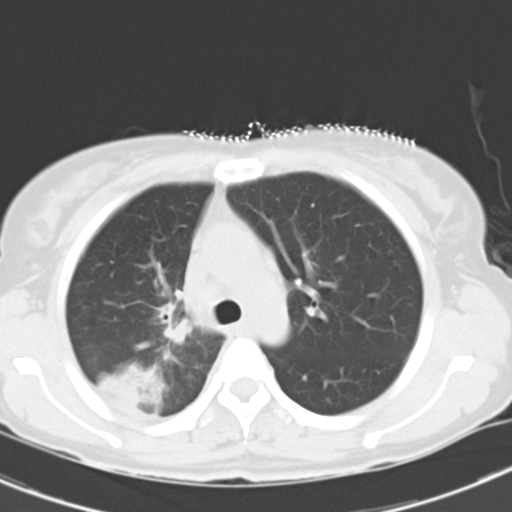
Chest CT, one axial slice. Position 21 of 29 along the scan axis. 120 kVp. Lung window (W 1500 / L -600 HU). 512 × 512 image matrix, field of view 300 × 300 mm. Patient: female, 47 years. From the clinical record (not read from this slice): clinical TNM (as recorded): T1c N3 M0.
Structures marked on this image (bounding box drawn by a radiologist):
- lung tumour (recorded histology: adenocarcinoma): bounding box (x1, y1, x2, y2) in pixels: (95, 359, 168, 403)